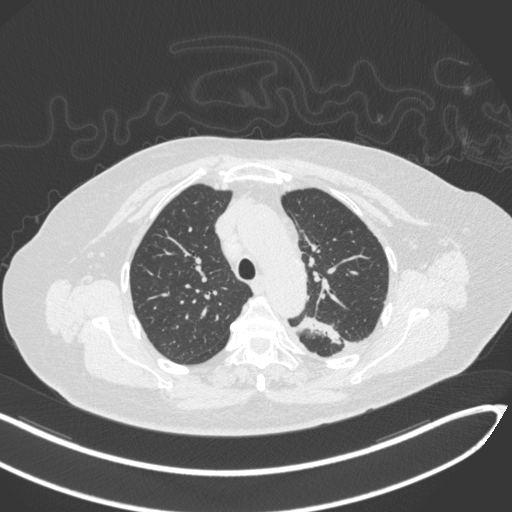
Chest CT, one axial slice; position 232 of 270 along the scan axis; reconstruction kernel B31f; 120 kVp; lung window (W 1500 / L -600 HU); 512 × 512 image matrix, field of view 400 × 400 mm. Patient: female, 76 years. Case-level facts recorded for this patient, not image findings: clinical TNM (as recorded): T1c N0 M0.
Structures marked on this image (bounding box drawn by a radiologist):
- lung tumour (recorded histology: adenocarcinoma): box from (x=295, y=314) to (x=344, y=346) px